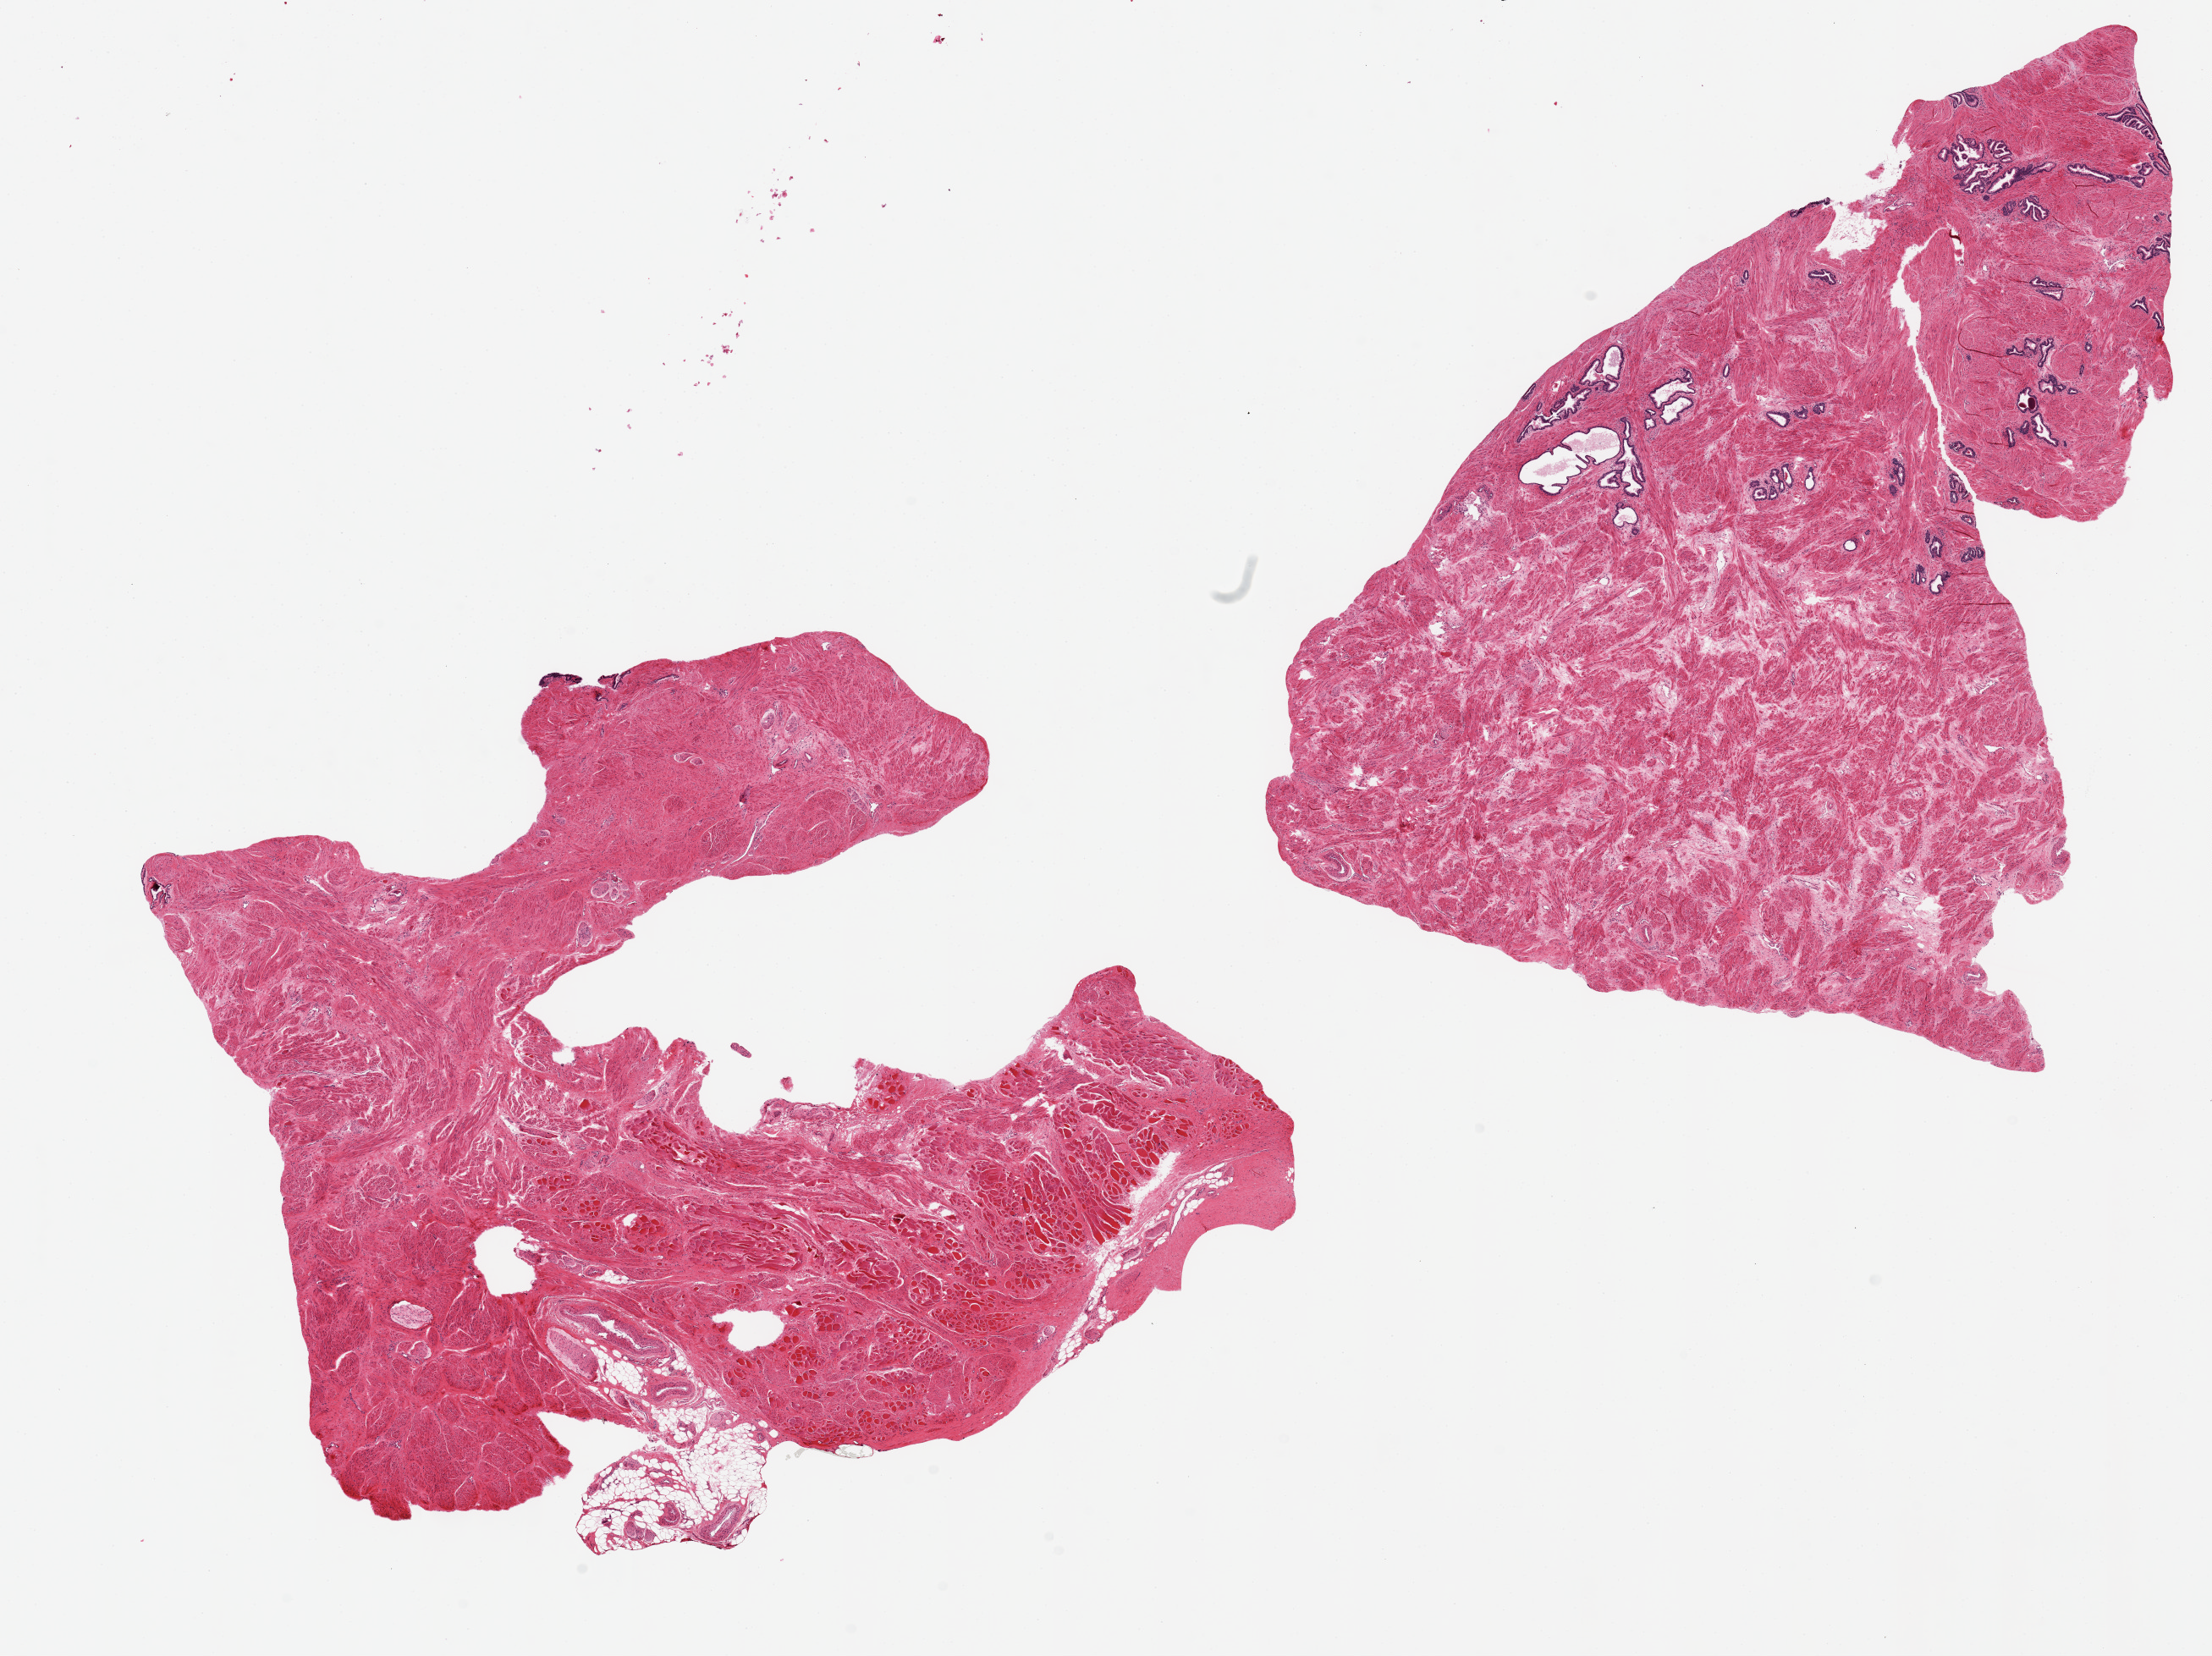
Digitized H&E-stained section, brightfield, shown as a low-resolution overview of the whole scanned area (about 20.7 x 15.5 mm). PAXgene-fixed paraffin-embedded (PFPE) section. Target tissue: prostate. Donor tissue sample.
Reviewer comment on this tissue sample: 2 pieces 10x7 & 8x8 mm; mostly fibromuscular hyperplasia; a few glands in one aliquot.